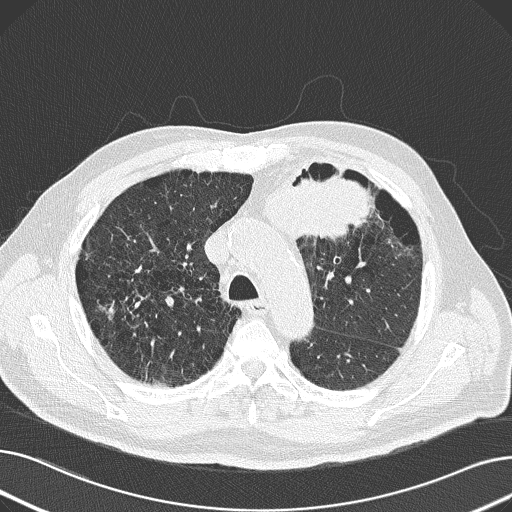
Low-dose screening chest CT, axial slice; baseline screening round; lung window (W 1500 / L -600 HU); 2 mm slice thickness; 120 kVp; slice 56 of 165 in the series. Male, age 69 years at enrolment. Former smoker at enrolment.
• Expert-annotated lung lesion, bounding box (x1, y1, x2, y2) in pixels: (227, 147, 380, 254).
• The exam's reader record, not a measurement of the box and not confirmed to be the same lesion: non-calcified nodule or mass ≥4 mm, left upper lobe, 6 × 10 mm, spiculated (stellate) margins, soft tissue attenuation.
• Later outcome: lung cancer diagnosed 20 days after this screen — non-small cell carcinoma, left upper lobe, poorly differentiated (G3), stage IB (AJCC 6th edition), 100 mm at pathology.